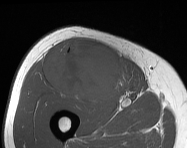
MRI of an extremity soft-tissue mass, one axial slice; position 79 of 114 along the scan axis; MR volume resampled by the dataset authors to the PET/CT grid (not the native acquisition matrix); 3.27 mm slice thickness; 187 × 148 image matrix. Male patient. From the clinical record (not read from this slice): histological type: pleiomorphic leiomyosarcoma; grade: intermediate; site of the primary tumour: right thigh.
Structures marked on this image (expert contour drawn on MRI and transferred to this co-registered scan by the dataset authors):
- gross tumour volume including surrounding oedema: bounding box <45,40,130,101> (left, top, right, bottom; pixels)
- gross tumour volume (mass): <45,40,130,101>